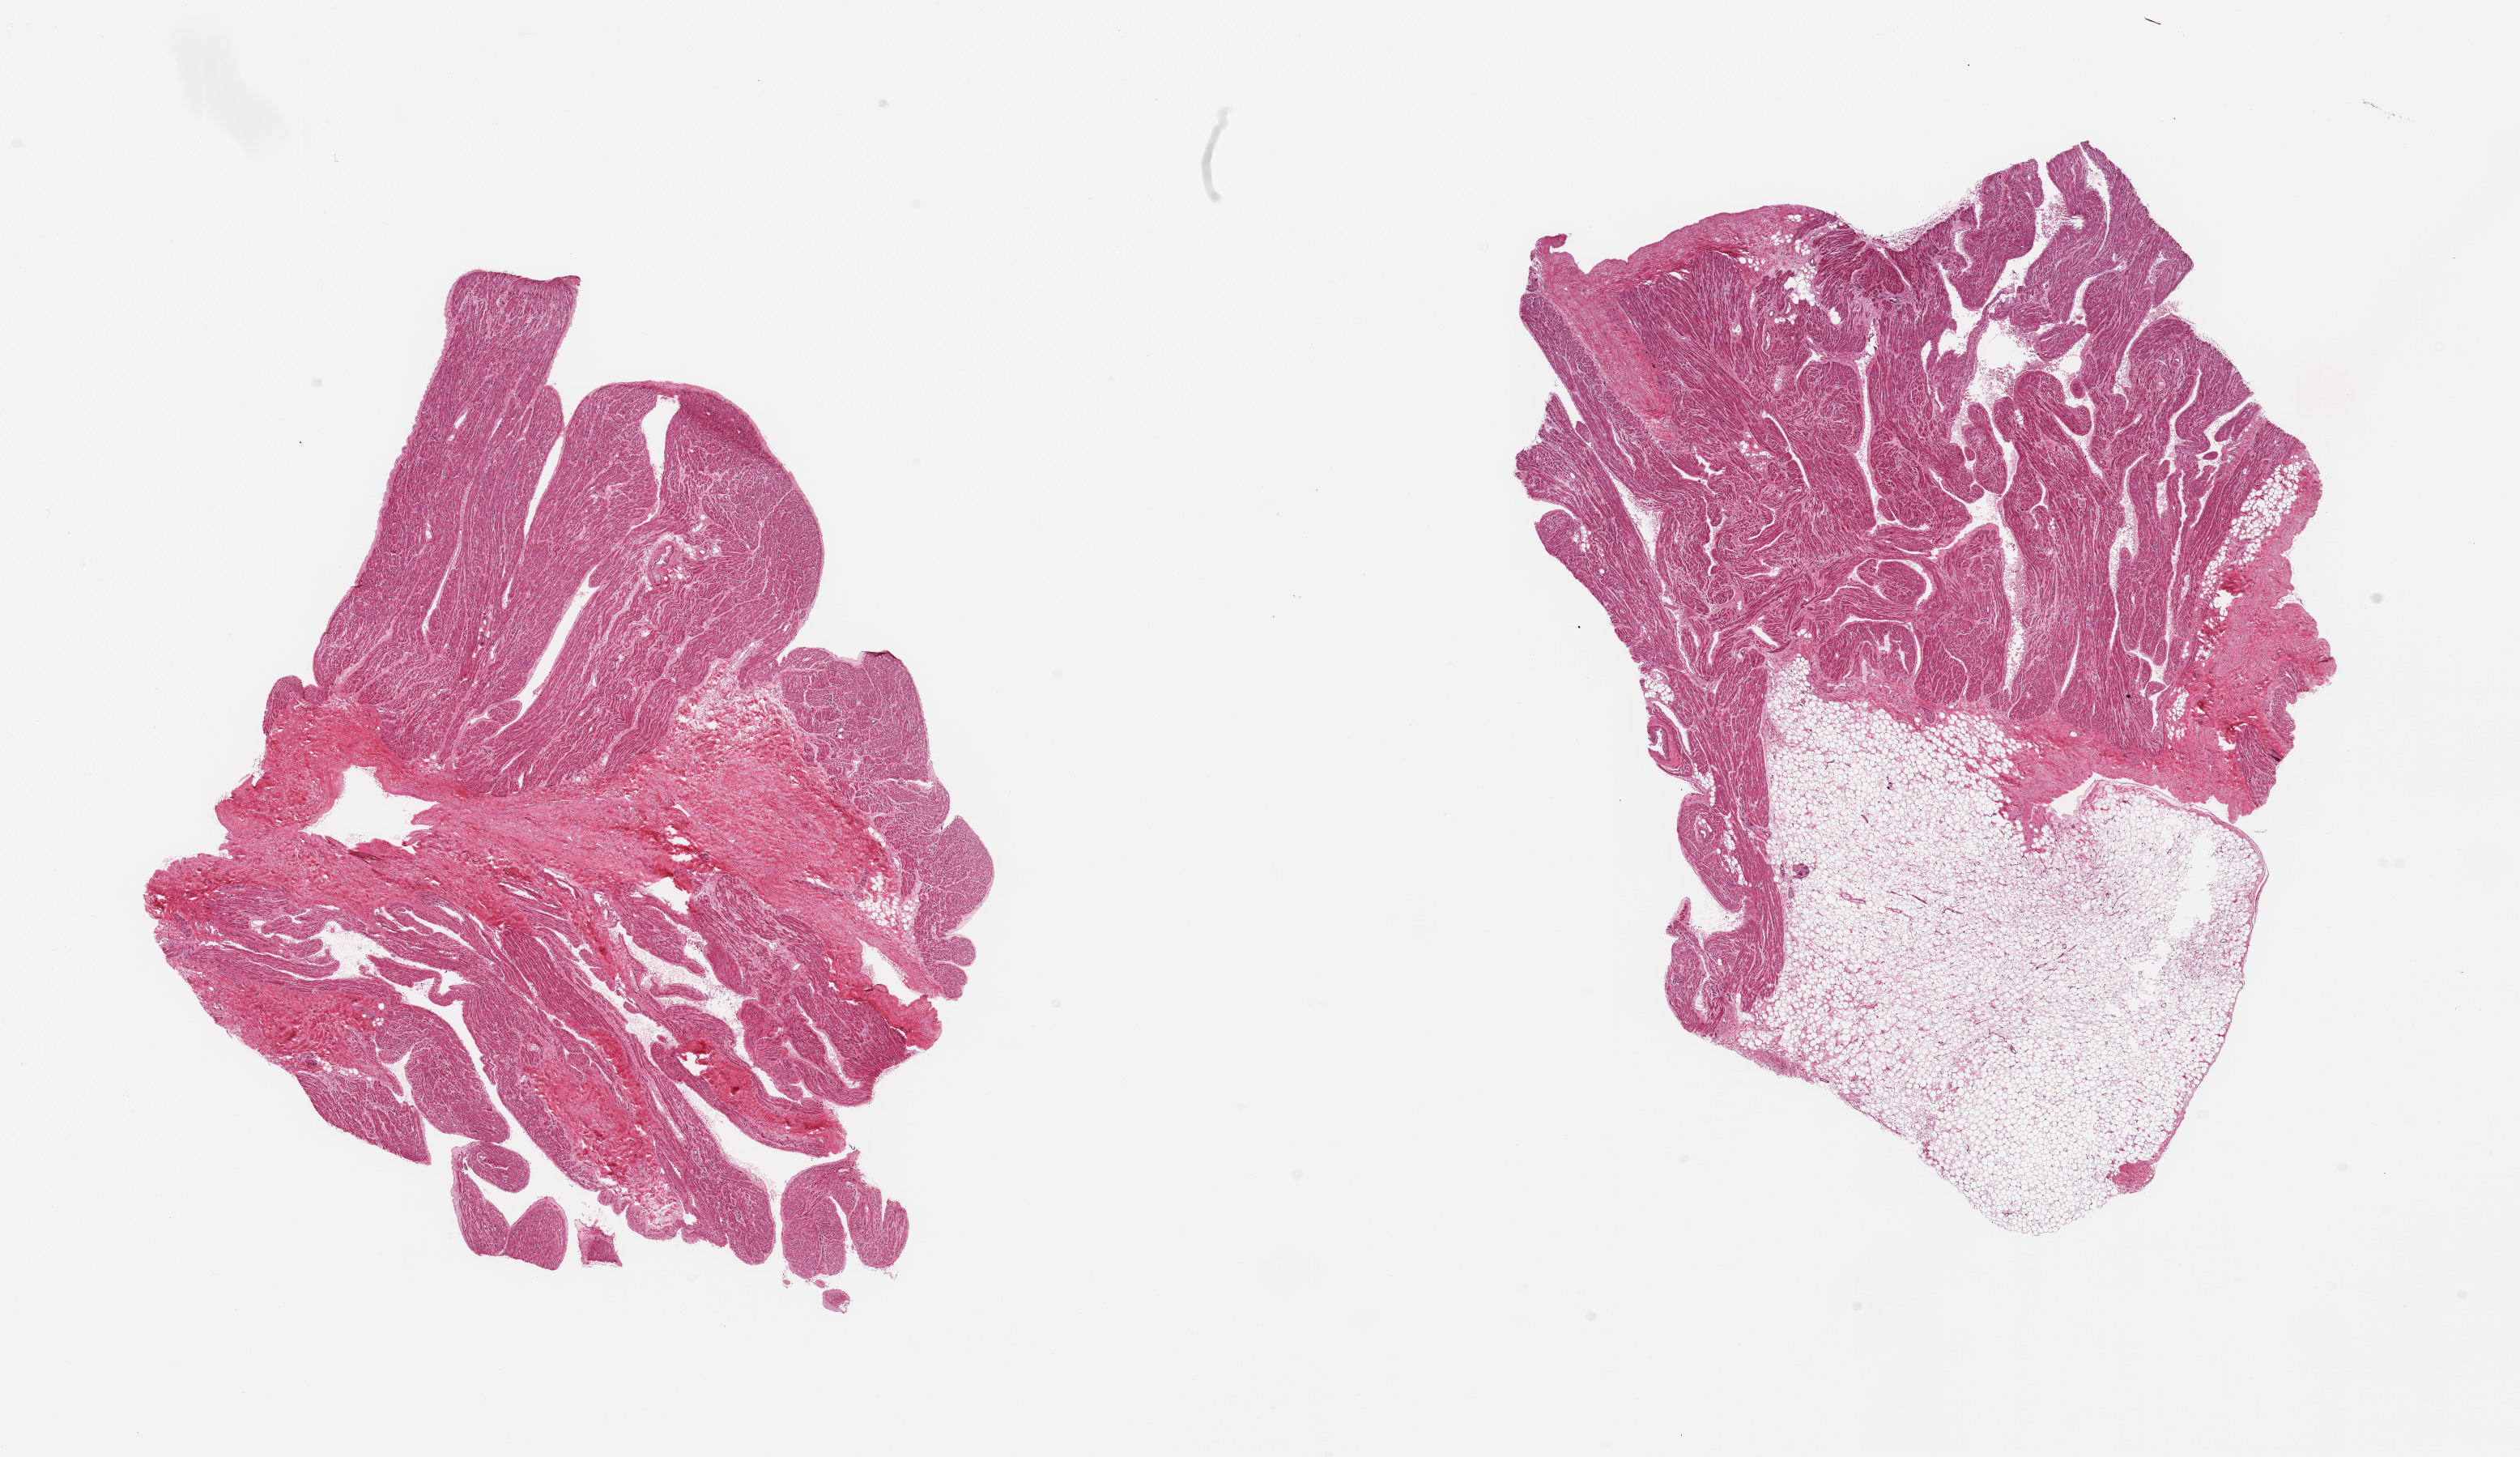
Whole-slide image, H&E stain, brightfield, shown as a low-resolution overview of the whole scanned area (about 24.6 x 14.2 mm); PAXgene-fixed paraffin-embedded (PFPE) section; section of auricular appendage (target tissue); donor tissue sample. Donor: male.
Pathologist's review note for this sample: 2 pieces, adherent fat is ~20% total specimen.